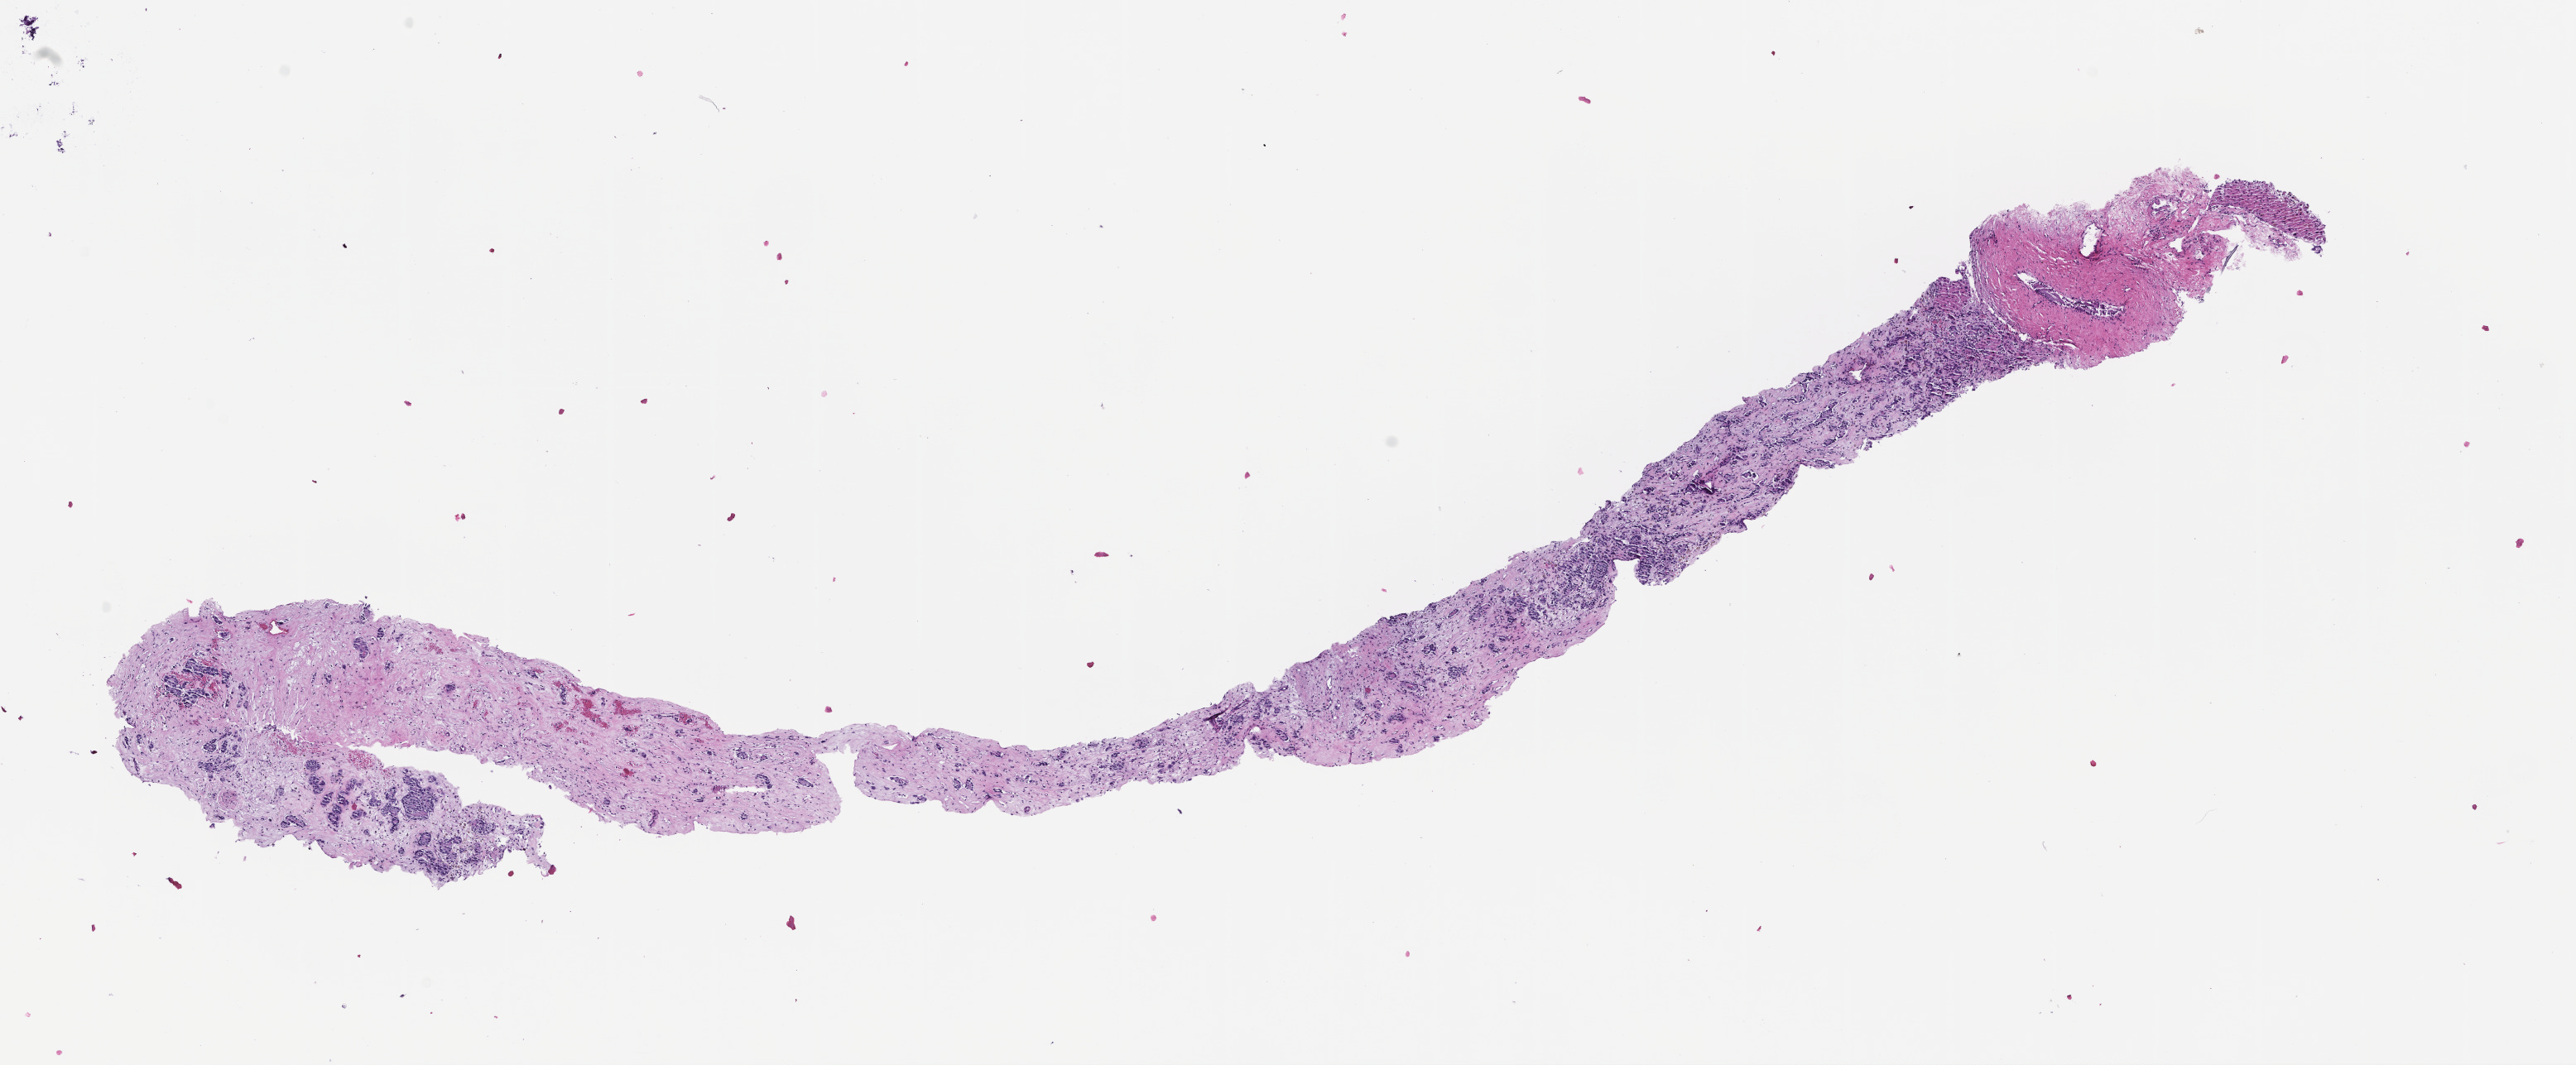
Digitized H&E-stained section, low-resolution overview of the scanned area, about 12.6 x 5.2 mm; FFPE section; specimen time point: collected at baseline (before treatment). Patient: male.
This section: metastasis (sampled organ not recorded). Primary diagnosis of the patient: Prostate Carcinoma.